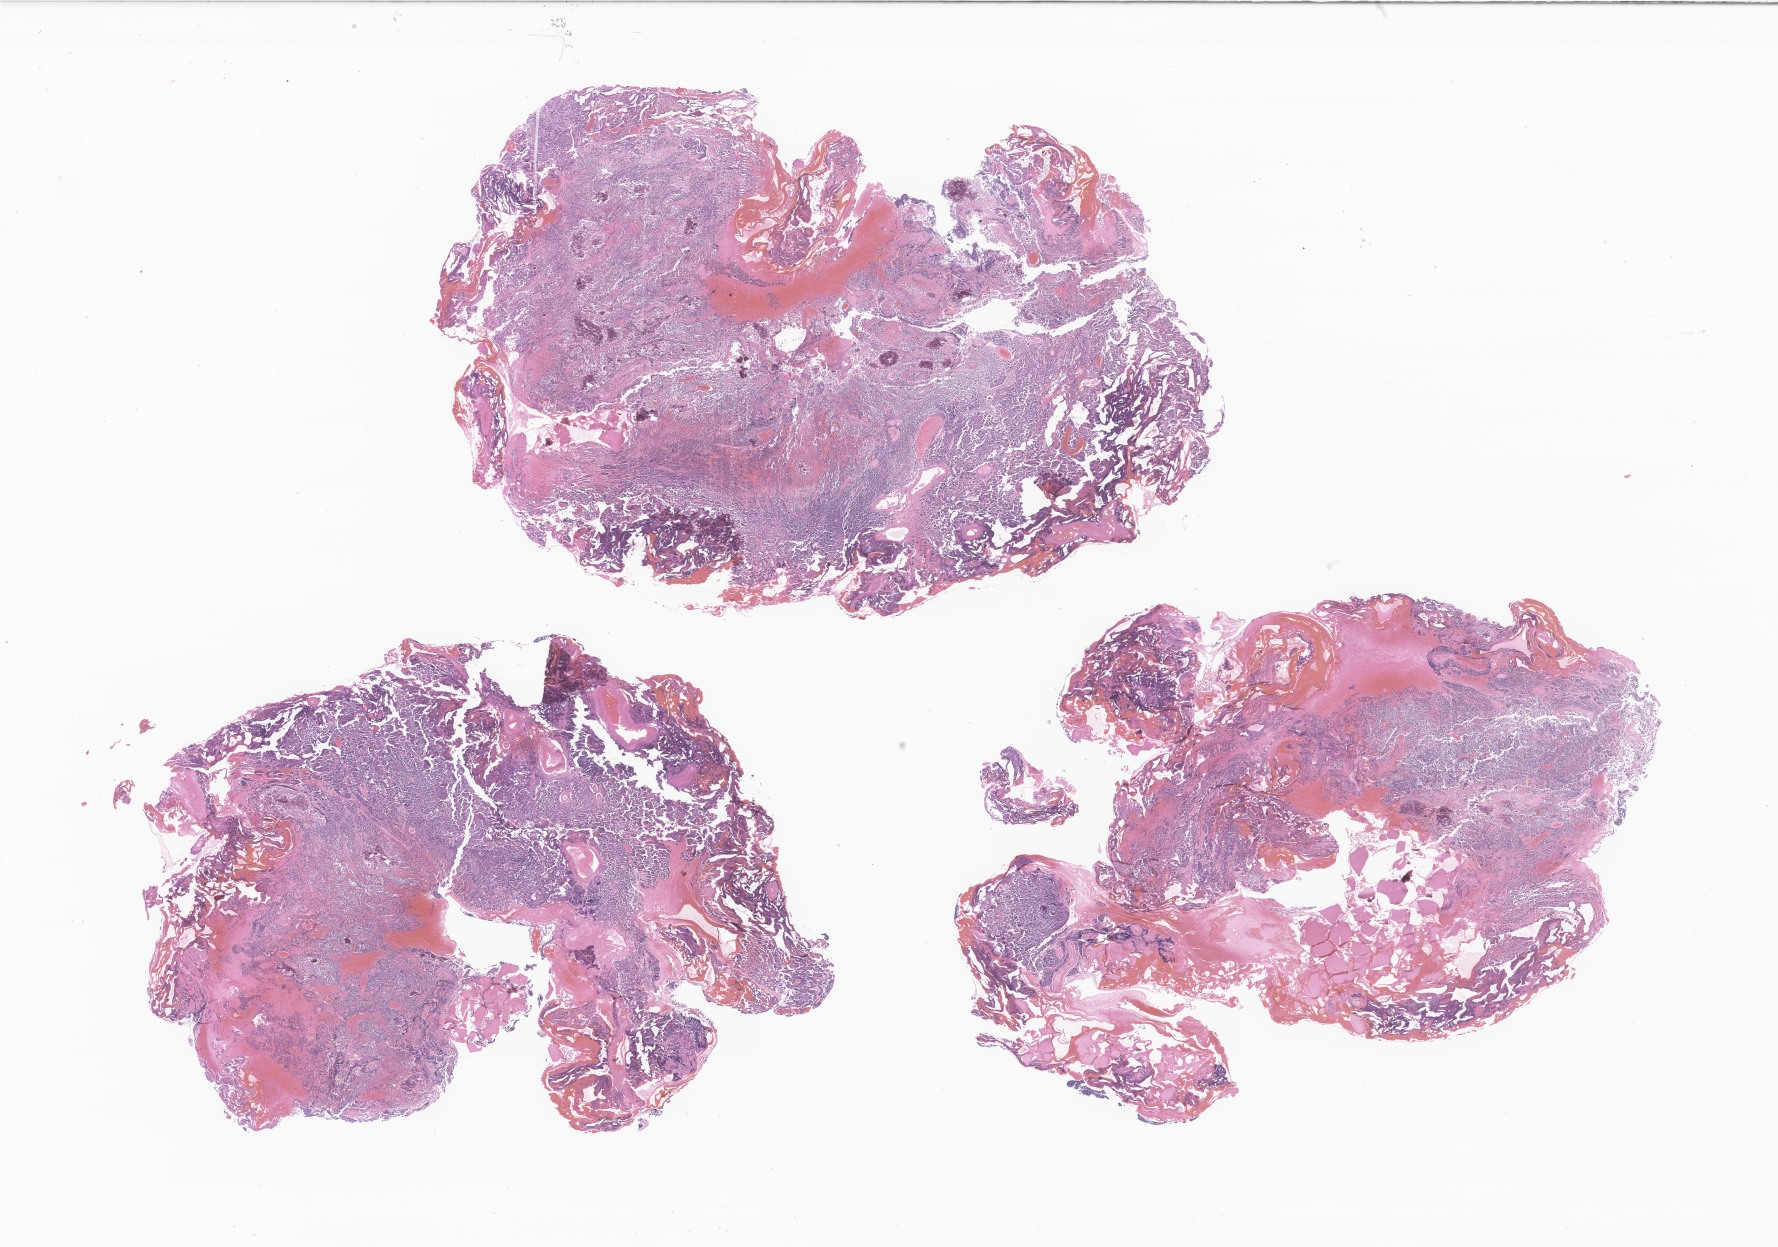
Whole-slide image, haematoxylin and eosin stain of tumor tissue from the pineal gland — whole scanned area (about 30.0 x 21.0 mm) shown as a low-resolution overview. FFPE section. Patient: female, age 62 months (5 years 2 months).
Diagnosis (ICD-O-3 morphology term): Pineoblastoma.